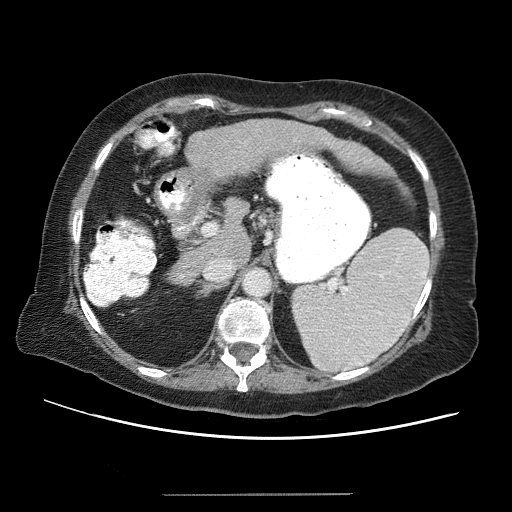
Contrast-enhanced abdominal CT (liver protocol), one axial slice; position 33 of 65 along the scan axis; reconstruction kernel STANDARD; soft-tissue window (W 400 / L 40 HU); 512 × 512 image matrix, field of view 380 × 380 mm. Case-level facts recorded for this patient, not image findings: diagnosis: hepatocellular carcinoma (patient treated with transarterial chemoembolisation; whether this scan precedes or follows treatment is not stated here); TNM stage (as recorded): Stage-IIIB; Child-Pugh class: A.
Annotated regions visible in this slice (semi-automatically segmented with operator editing):
- liver parenchyma outside the tumour (the mass and vessels are separate outlines, so this box may not span the whole liver): bounding box [x1, y1, x2, y2] px = [164, 120, 412, 286]
- liver vessels: [194, 136, 374, 255]